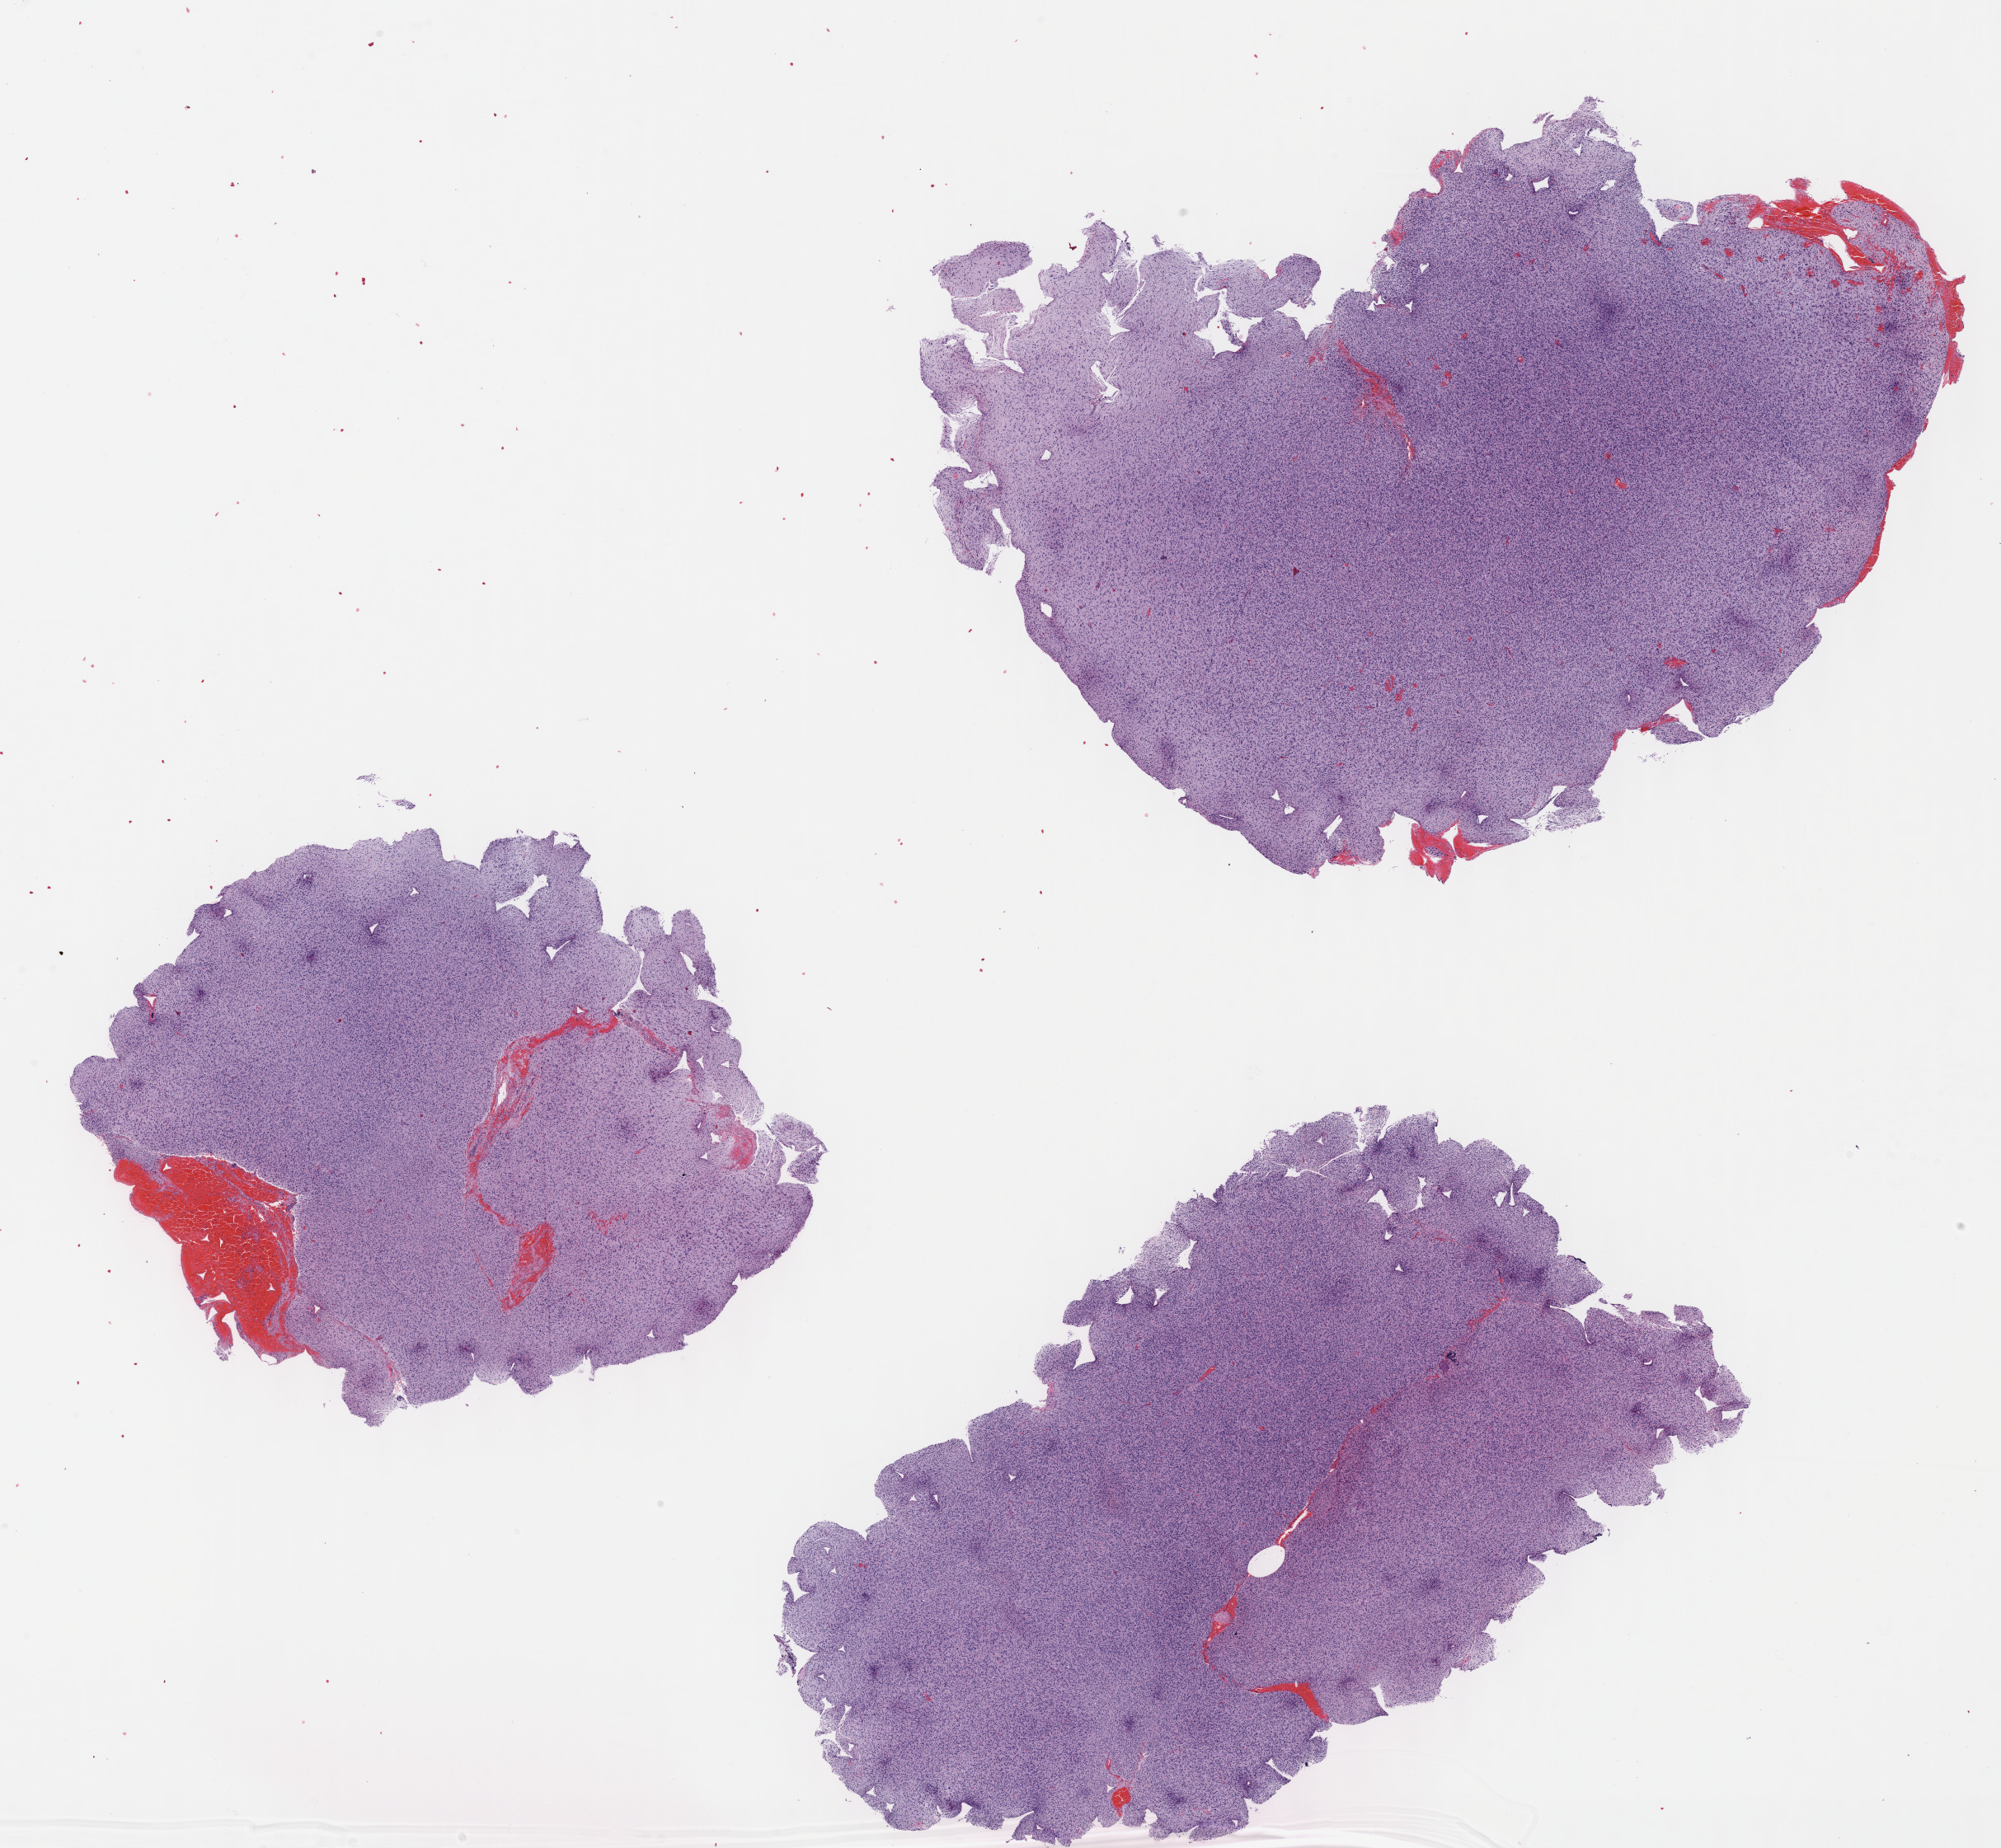
Digitized H&E-stained tissue section (whole slide) — a low-resolution overview of the entire scanned area, about 19.6 x 18.1 mm (from a 40x scan). FFPE section. Sample: primary tumour, brain. Patient: female, age at initial diagnosis 45 years. Histologic grade: G3 (poorly differentiated).
Pathologic diagnosis: Astrocytoma, anaplastic (cerebrum). Laterality: right.